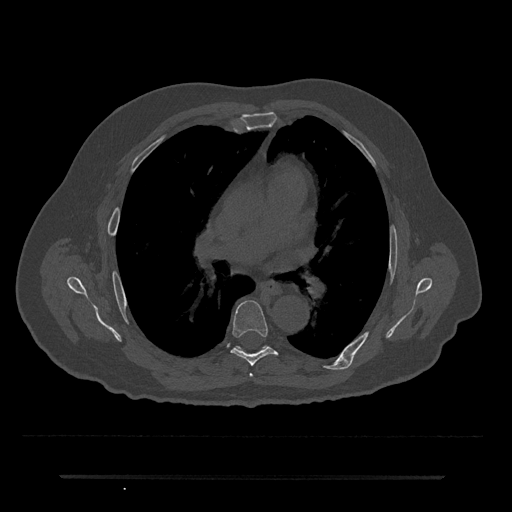
CT including the spine, one axial slice; position 430 of 797 along the scan axis; reconstruction kernel Br40s/3; 120 kVp; bone window (W 1800 / L 400 HU); 0.5 mm slice thickness; 512 × 512 image matrix. Patient: male, 69 years. From the clinical record (not read from this slice): primary cancer: prostate.
Annotated regions visible in this slice (semi-automatic segmentation, software-assisted and operator-edited):
- T5 vertebra: bounding box [x1, y1, x2, y2] px = [250, 374, 253, 377]
- T6 vertebra: [231, 301, 278, 366]